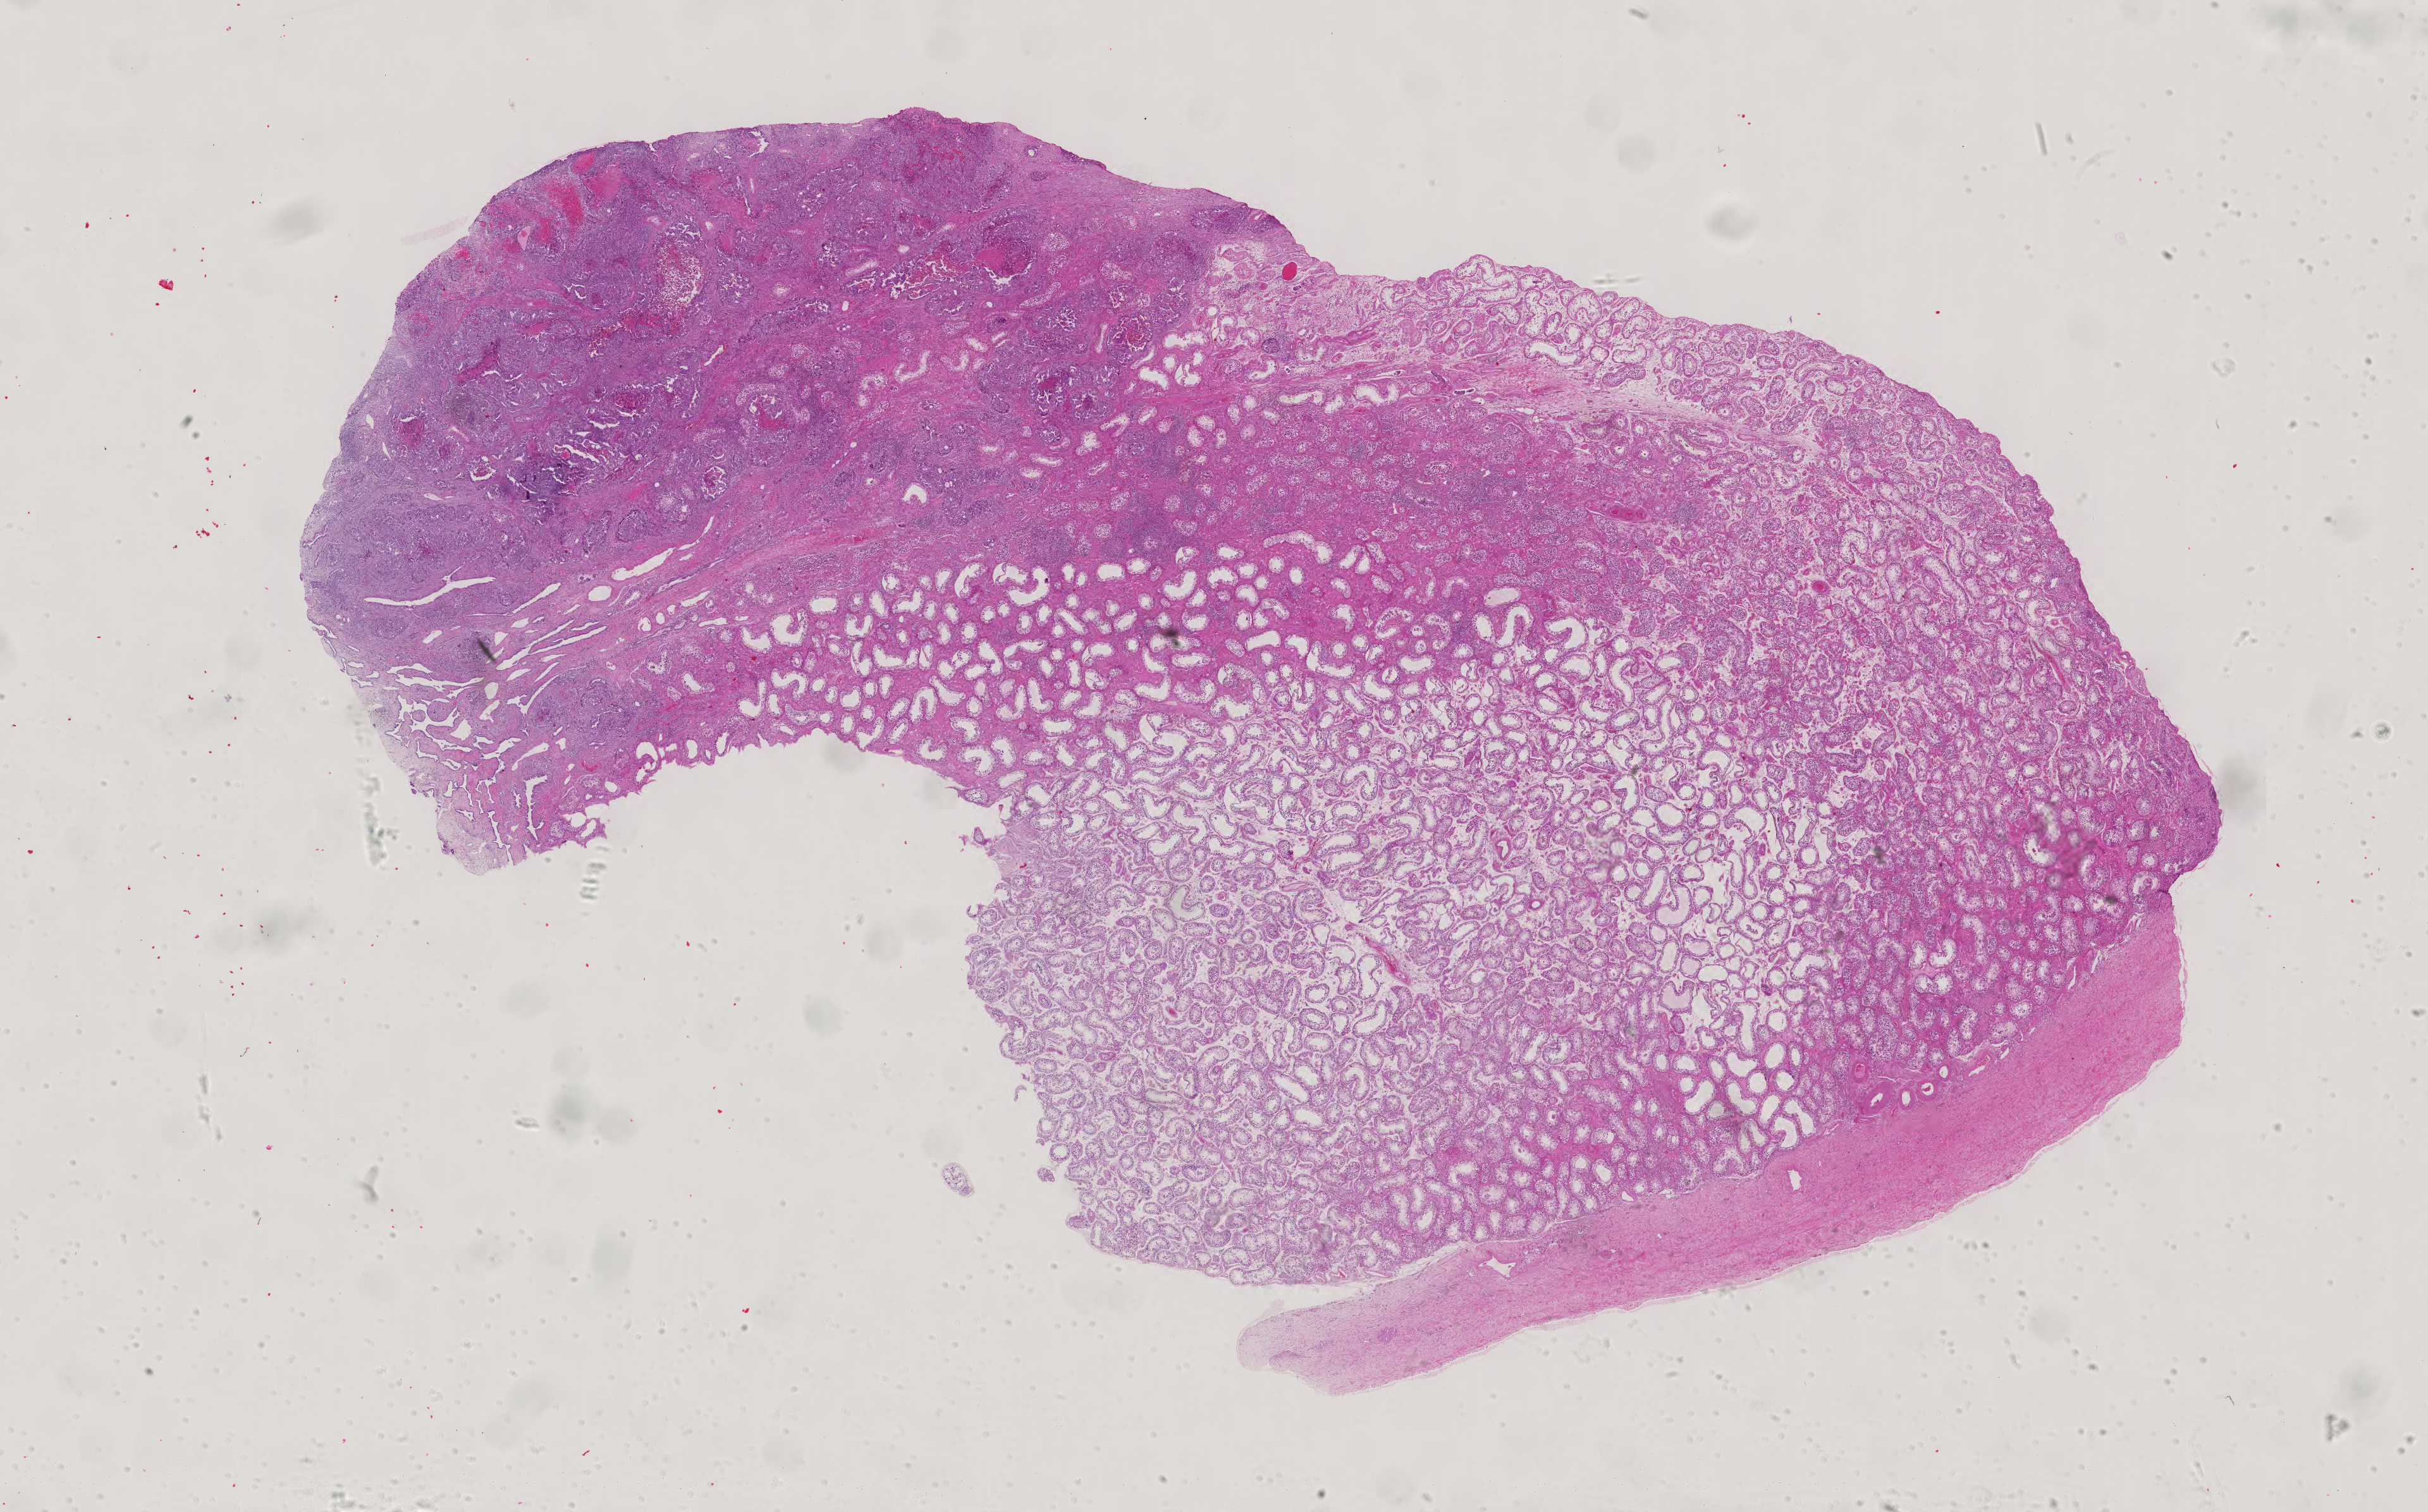
Whole-slide histology image, H&E, whole scanned area (about 28.0 x 17.4 mm, from a 40x scan) shown as a low-resolution overview. FFPE section. Primary tumour sample from the testis. Patient: male, age at initial diagnosis 41 years.
Pathologic diagnosis: Embryonal carcinoma, NOS.